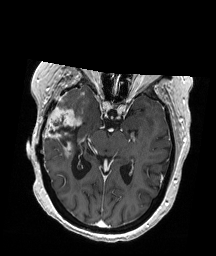
Brain MRI from a brain-tumour surgery series, one axial slice. Slice 114 of 192 in the series (ordered by position). T1-weighted post-contrast. 1 mm slice thickness. 216 × 256 image matrix, field of view 211 × 250 mm. From the clinical record (not read from this slice): histopathology: Glioblastoma; WHO grade: 4; IDH mutation: no.
Annotated regions visible in this slice (manually delineated by an expert):
- tumour: bounding box <43,94,83,158> (left, top, right, bottom; pixels)